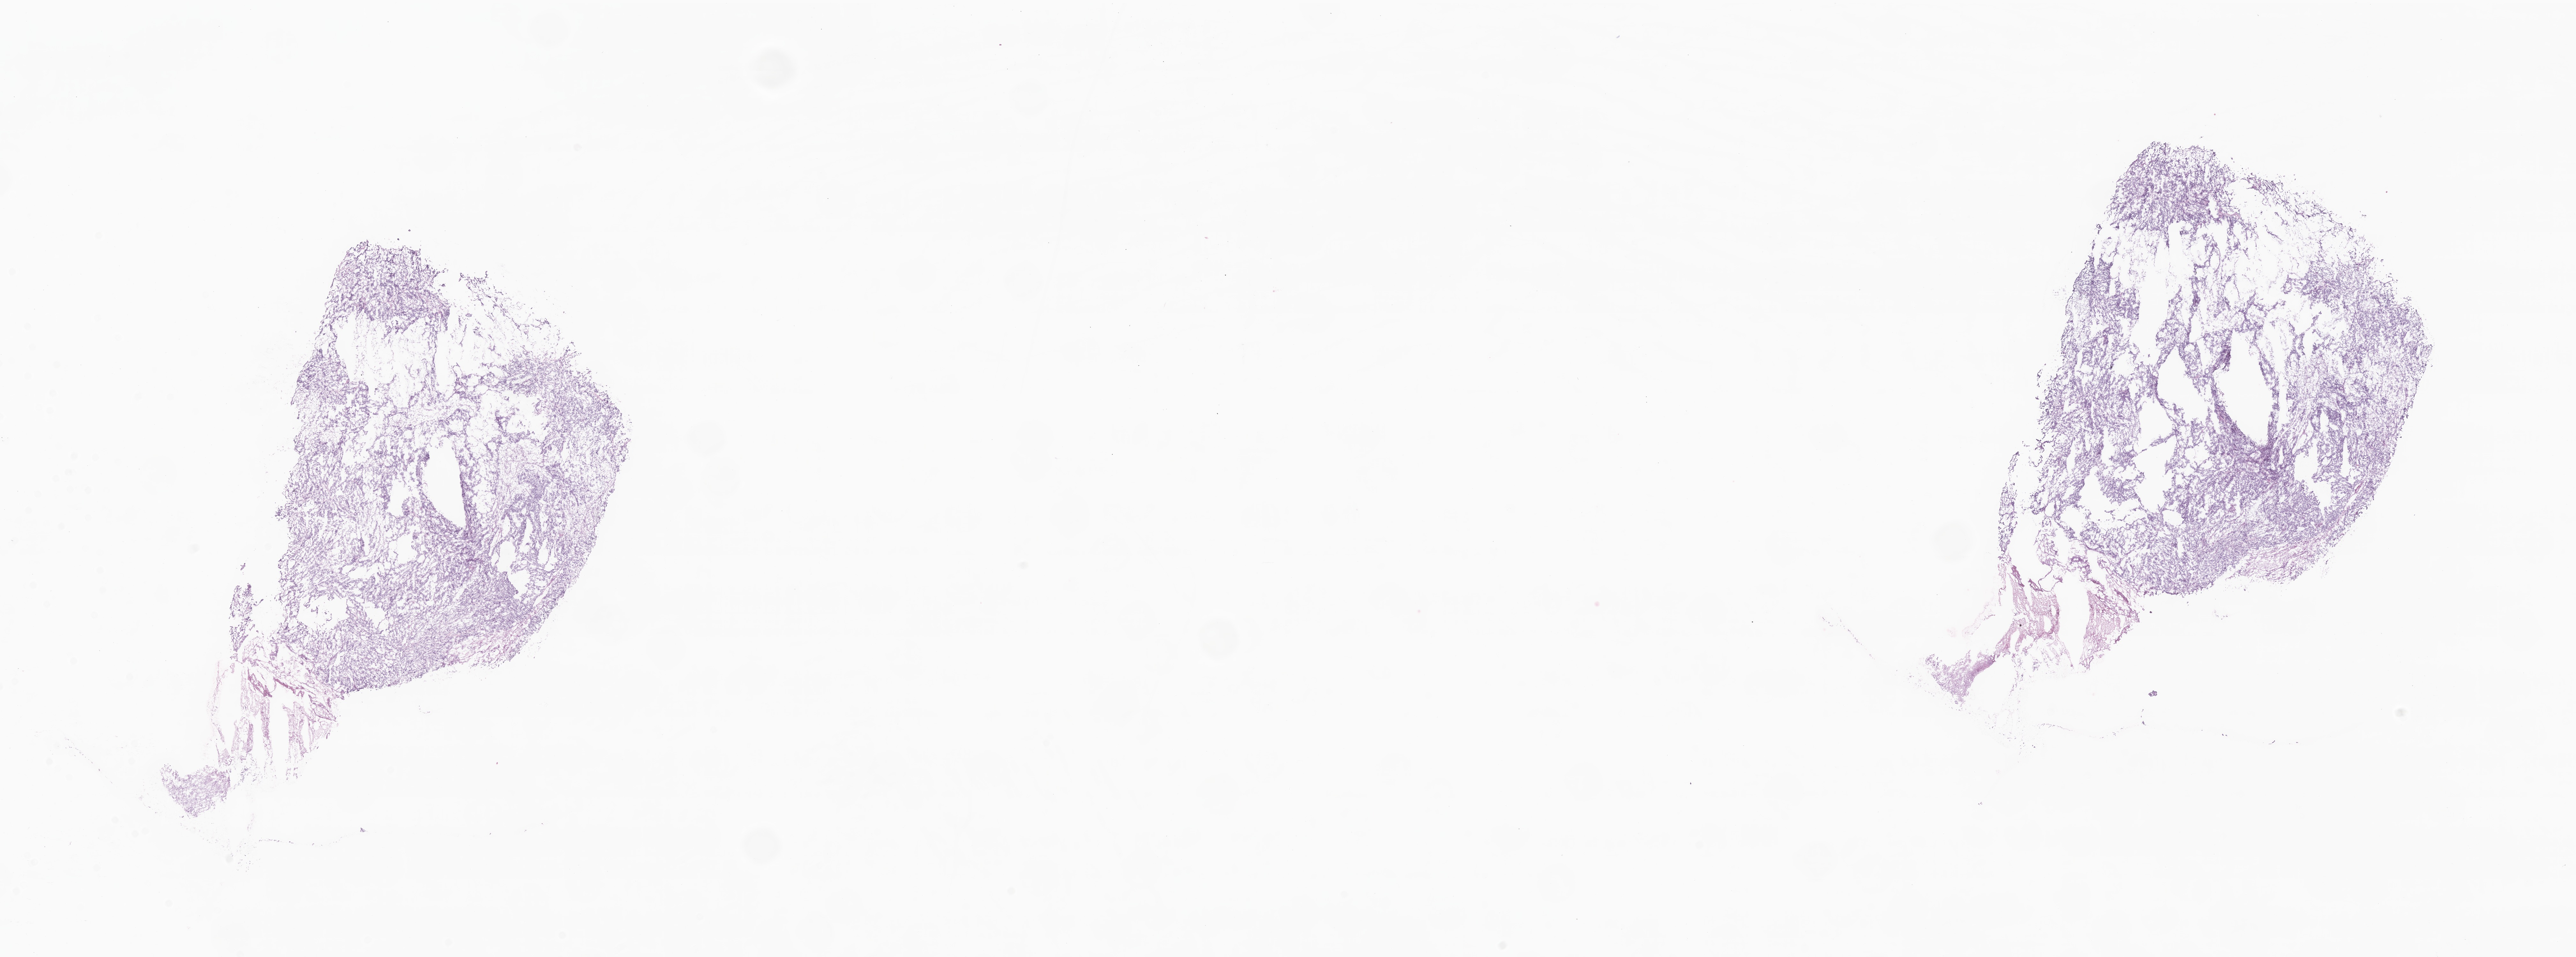
Digitized H&E-stained section of tumor tissue from the brain, a low-resolution overview of the entire scanned area, about 34.0 x 12.6 mm, frozen section (OCT-embedded). Female patient, age 336 days.
Recorded diagnosis: Neoplasm, metastatic.